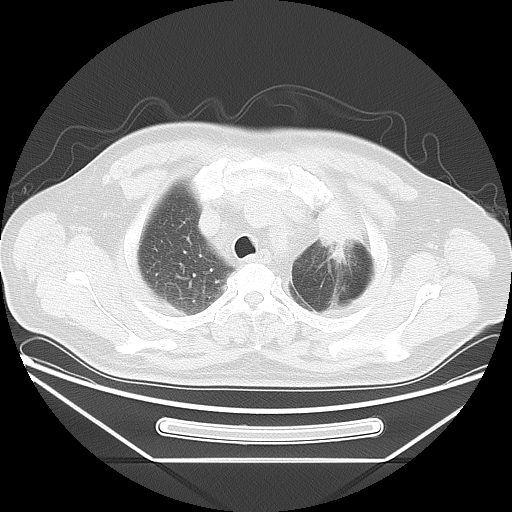
Chest CT, one axial slice. Slice 33 of 37 in the series (ordered by position). Reconstruction kernel LUNG. 120 kVp. Lung window (W 1500 / L -600 HU). 5 mm slice thickness. 512 × 512 image matrix, field of view 411 × 411 mm. Male patient, age 61 years. From the clinical record (not read from this slice): clinical TNM (as recorded): T2a N0 M0.
Structures marked on this image (rectangle marked by the reading radiologist):
- lung tumour (recorded histology: small cell carcinoma): box from (x=315, y=191) to (x=366, y=273) px